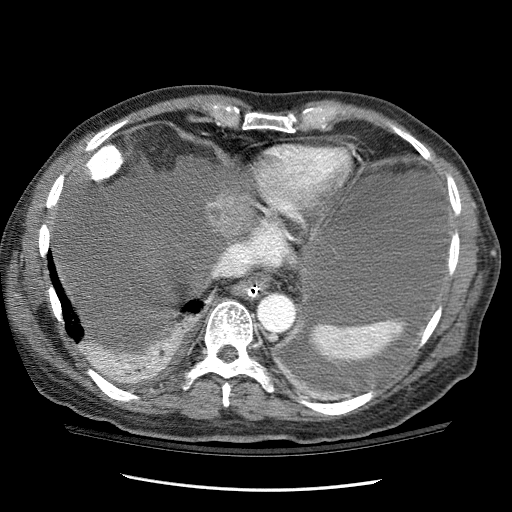
Contrast-enhanced abdominal CT (liver protocol), one axial slice; position 97 of 114 along the scan axis; 120 kVp; one of 3 acquisitions stored at this slice position; soft-tissue window (W 400 / L 40 HU); 512 × 512 image matrix, field of view 360 × 360 mm. Case-level facts recorded for this patient, not image findings: diagnosis: hepatocellular carcinoma (patient treated with transarterial chemoembolisation; whether this scan precedes or follows treatment is not stated here); TNM stage (as recorded): Stage-I; Child-Pugh class: C; tumour differentiation: well differentiated; tumour nodularity: uninodular.
Annotated regions visible in this slice (semi-automatically segmented with operator editing):
- liver parenchyma outside the tumour (the mass and vessels are separate outlines, so this box may not span the whole liver): bounding box <78,334,180,383> (left, top, right, bottom; pixels)
- mass: <205,194,253,237>
- liver vessels: <100,343,169,378>